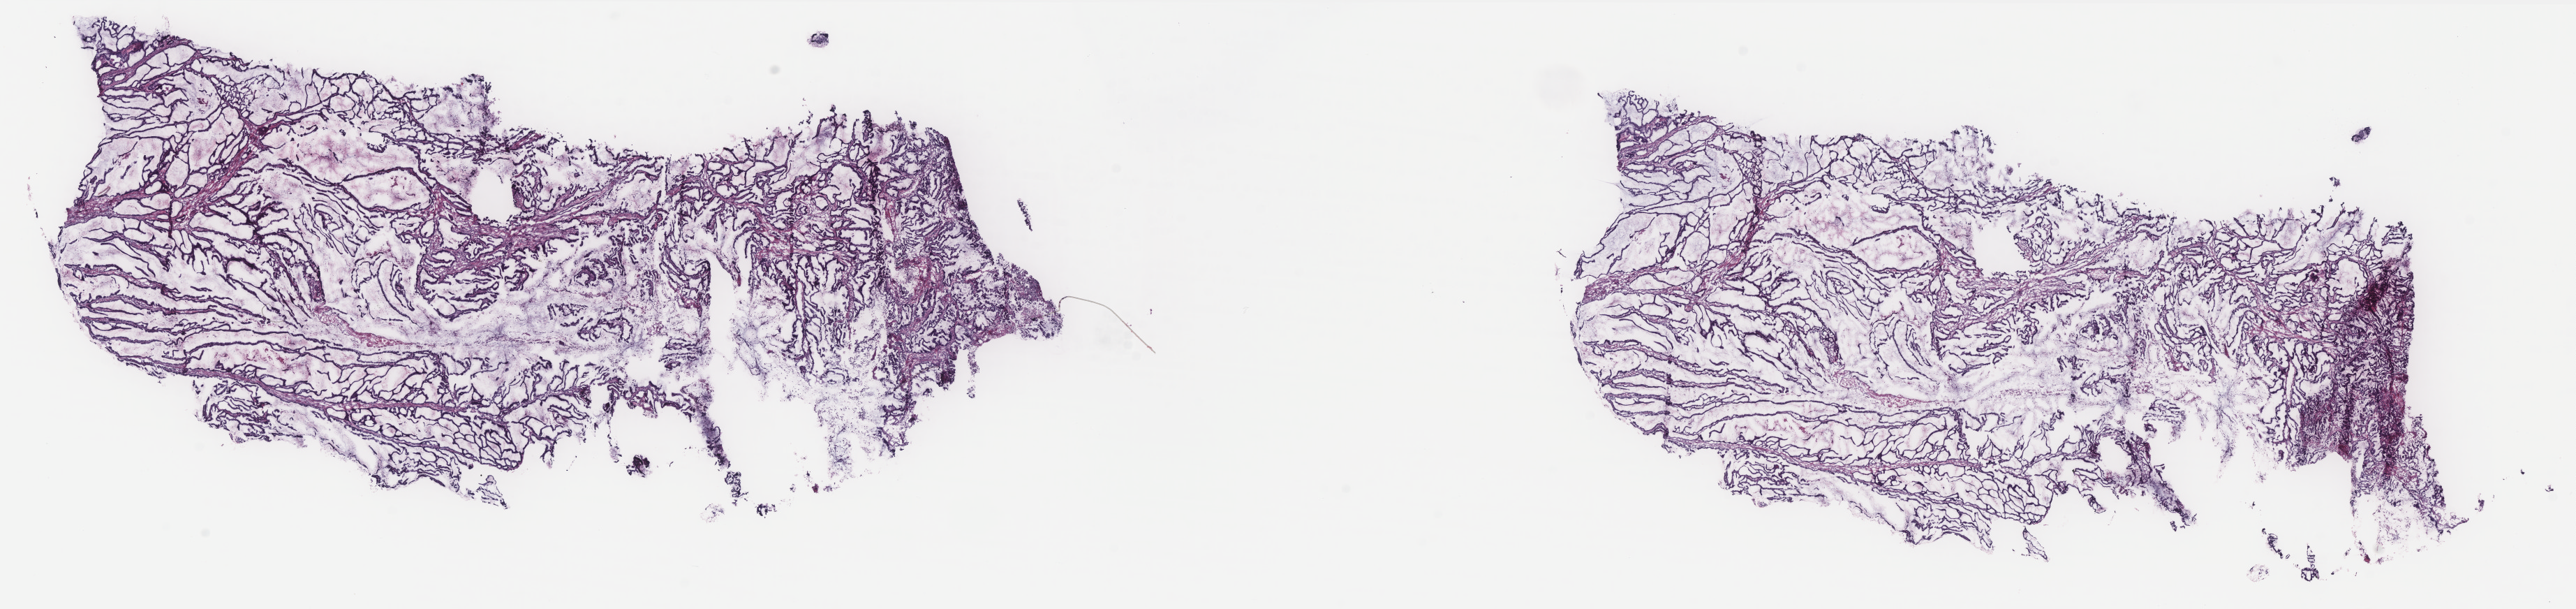
Whole-slide histology image, Hematoxylin and eosin (H&E) stained — low-resolution overview of the scanned area, about 29.6 x 7.0 mm, frozen section, uterus, primary tumour sample. Female patient; age at initial diagnosis 56 years. Histologic grade: G1 (well differentiated). Slide review estimates, as recorded: tumour cells 70%, tumour nuclei 70%, normal cells 0%, stromal cells 25%, necrosis 5%. Inflammatory infiltration, as recorded: lymphocyte infiltration 40%, monocyte infiltration 20%, neutrophil infiltration 20%.
Histologic diagnosis: Endometrioid adenocarcinoma, NOS. Lymph nodes positive (case pathology): 0 of 2 examined. FIGO stage: IB.